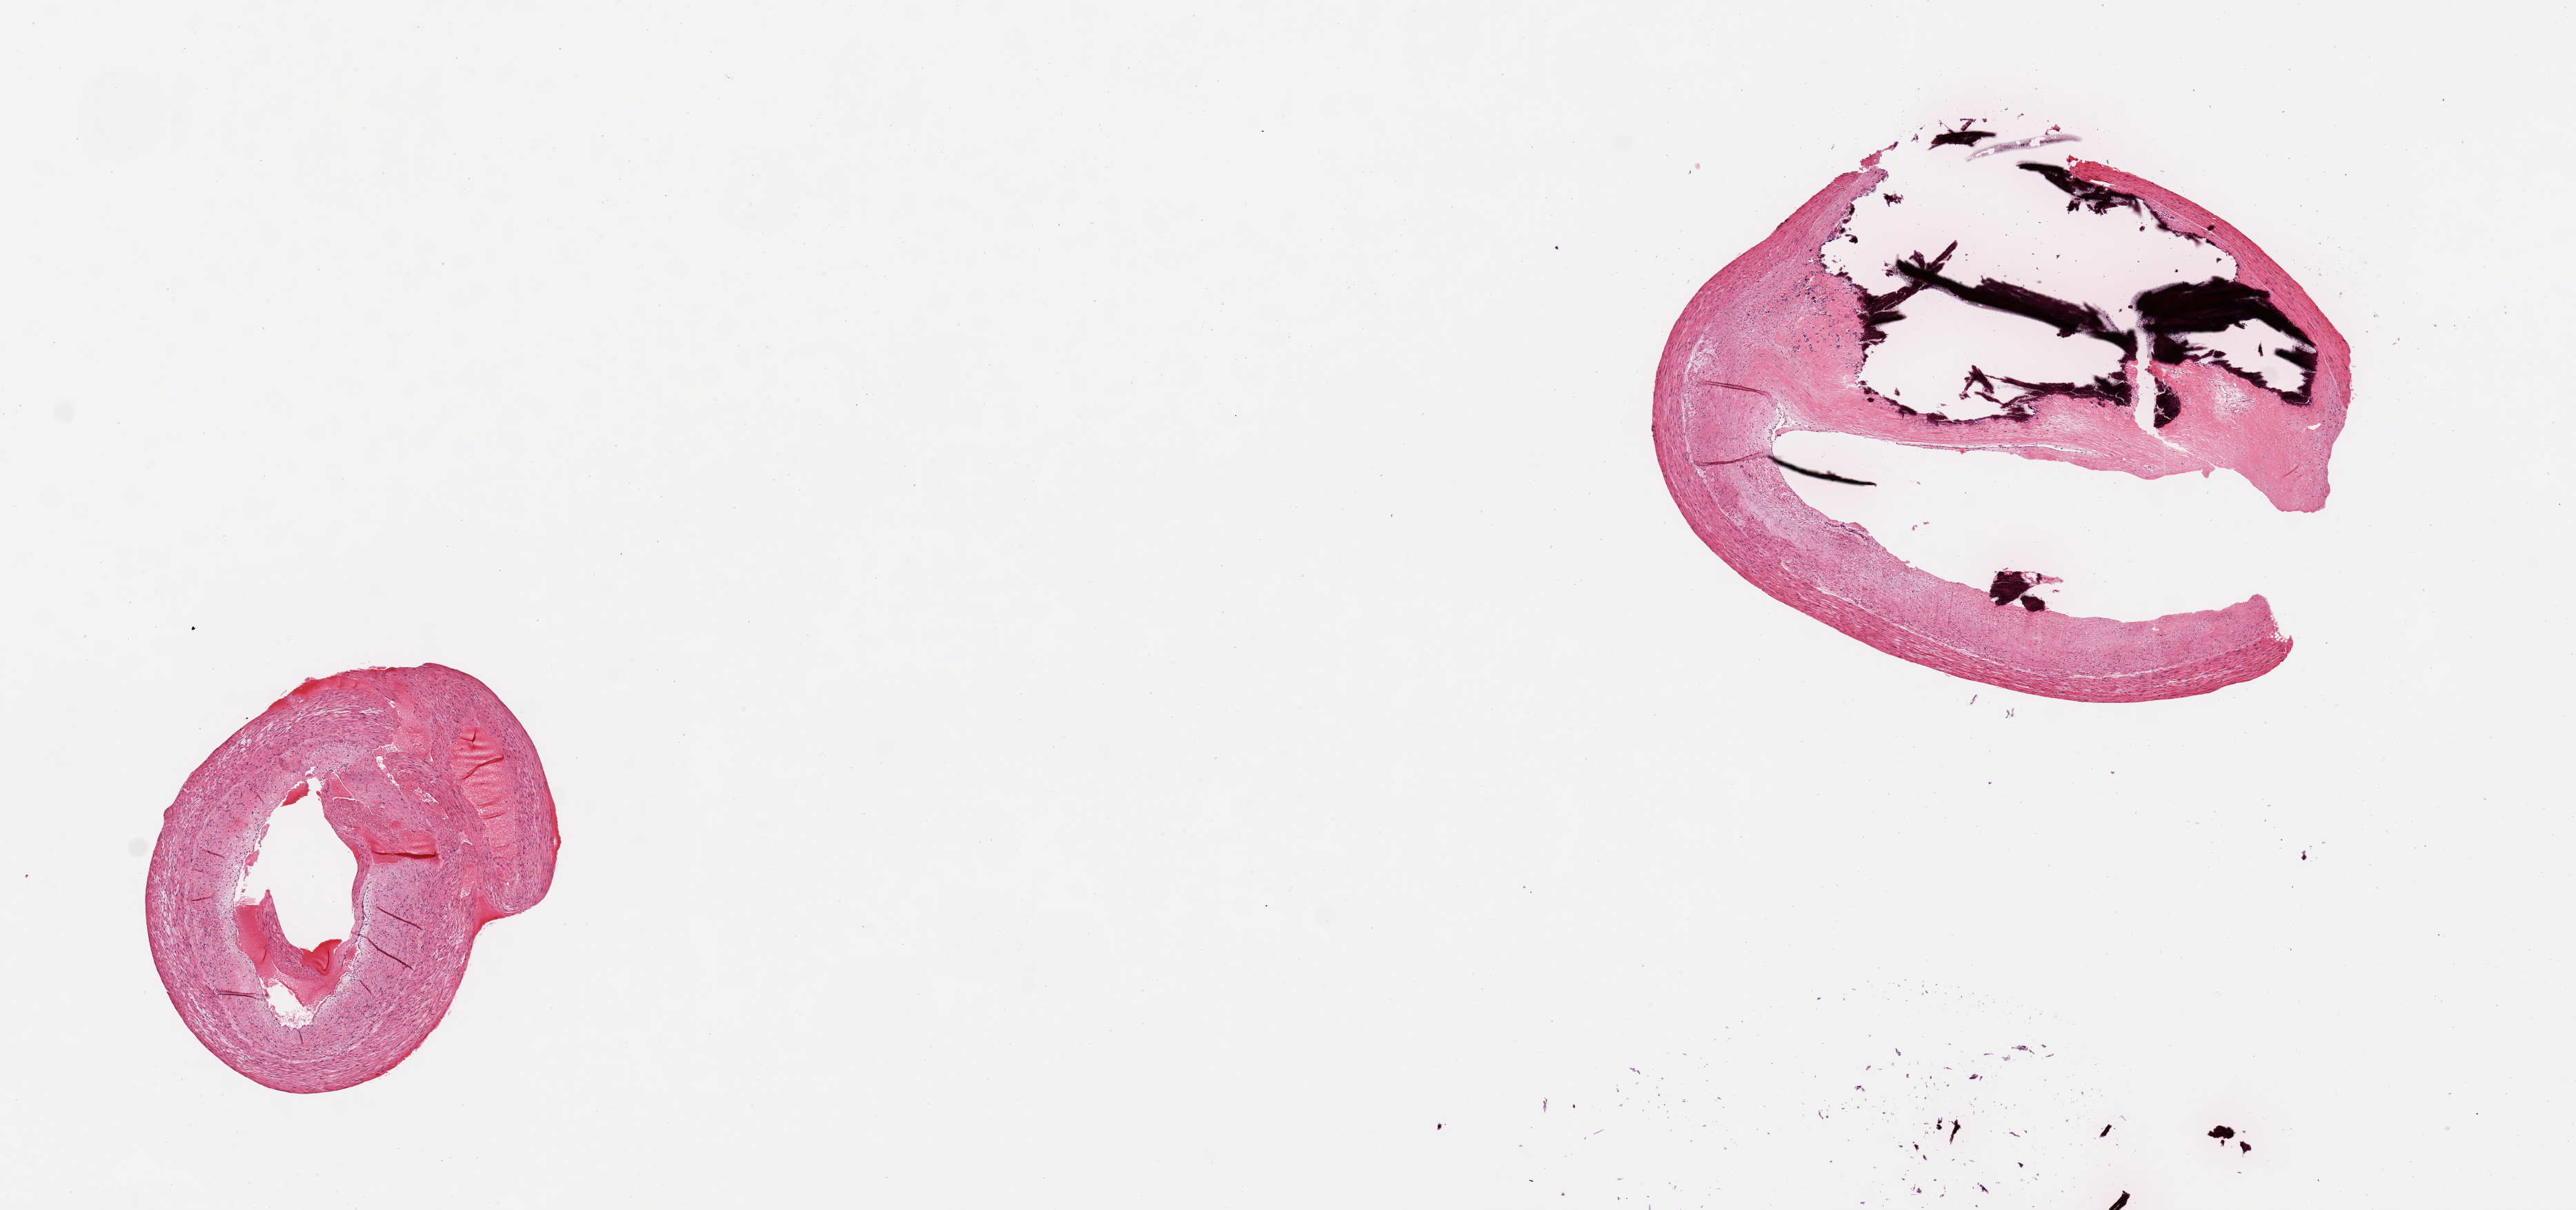
Digitized haematoxylin and eosin-stained section — shown as a low-resolution overview of the whole scanned area (about 14.8 x 6.9 mm); PAXgene-fixed paraffin-embedded (PFPE) section; sampled site (target tissue): coronary artery; tissue donor sample. Donor: female.
Review note (as recorded): 2 pieces, calcific atherosclerosis.